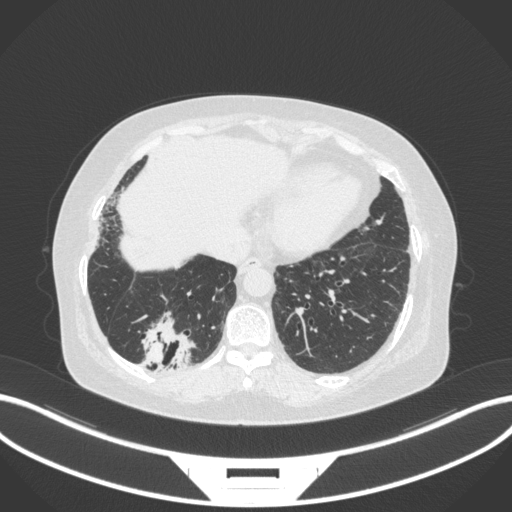
Chest CT, one axial slice; position 49 of 303 along the scan axis; 120 kVp; lung window (W 1500 / L -600 HU); 1 mm slice thickness; 512 × 512 image matrix, field of view 400 × 400 mm. Patient: female, 65 years. Case-level facts recorded for this patient, not image findings: clinical TNM (as recorded): T2b N1 M0; histopathological grade: G1.
Structures marked on this image (rectangle marked by the reading radiologist):
- lung tumour (recorded histology: adenocarcinoma): box from (x=138, y=309) to (x=198, y=374) px